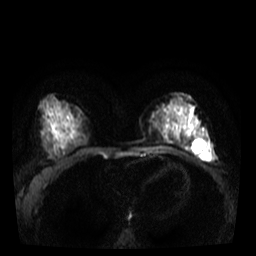
Breast MRI, one axial slice. Slice 17 of 40 in the series (ordered by position). Diffusion-weighted series; image 2 of 4 stored at this slice position (different b-values; order by instance number). 3 T. 5 mm slice thickness. 256 × 256 image matrix, field of view 320 × 320 mm. Female patient.
Structures marked on this image (outlined manually by an expert reader):
- tumour on diffusion-weighted imaging: box from (x=200, y=148) to (x=212, y=159) px